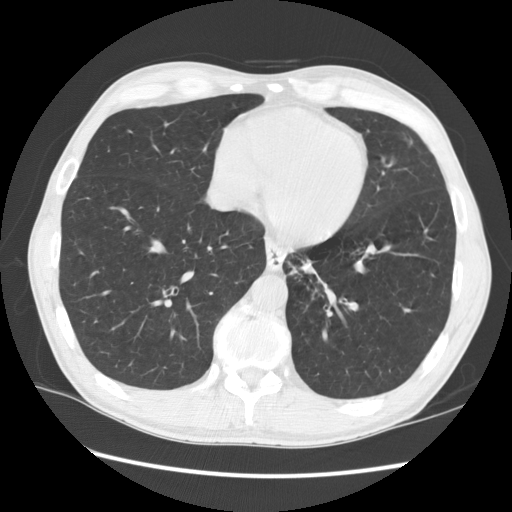
Axial slice from a low-dose chest CT screening exam, first (baseline) screen, lung window (W 1500 / L -600 HU), standard (soft-tissue) reconstruction kernel (STANDARD), 512 × 512 image matrix. Male participant, aged 57 years at enrolment. Current smoker at enrolment.
Expert reader's lesion annotation, bounding box [x1, y1, x2, y2] px = [269, 242, 338, 304]. The screening reader recorded 2 non-calcified nodules or masses ≥4 mm on this exam (left lower lobe, lingula); which of them this box marks is not recorded. Official screen result: positive, change unspecified: nodule(s) >= 4 mm or enlarging nodule(s), mass(es), or other non-specific abnormalities suspicious for lung cancer. Lung cancer was diagnosed 95 days after this screen: squamous cell carcinoma, NOS, left lower lobe, moderately differentiated (G2), stage IB (AJCC 6th edition), 35 mm at pathology.